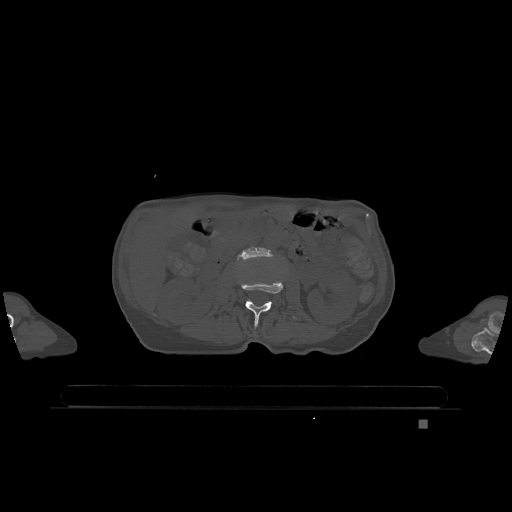
CT including the spine, one axial slice. Position 403 of 1317 along the scan axis. Bone window (W 1800 / L 400 HU). 512 × 512 image matrix. Female patient, age 74 years. From the clinical record (not read from this slice): primary cancer: lung.
Outlined on this slice (semi-automatically segmented with operator editing):
- L2 vertebra: box from (x=241, y=281) to (x=297, y=328) px
- L3 vertebra: (x=237, y=246)–(x=270, y=260)